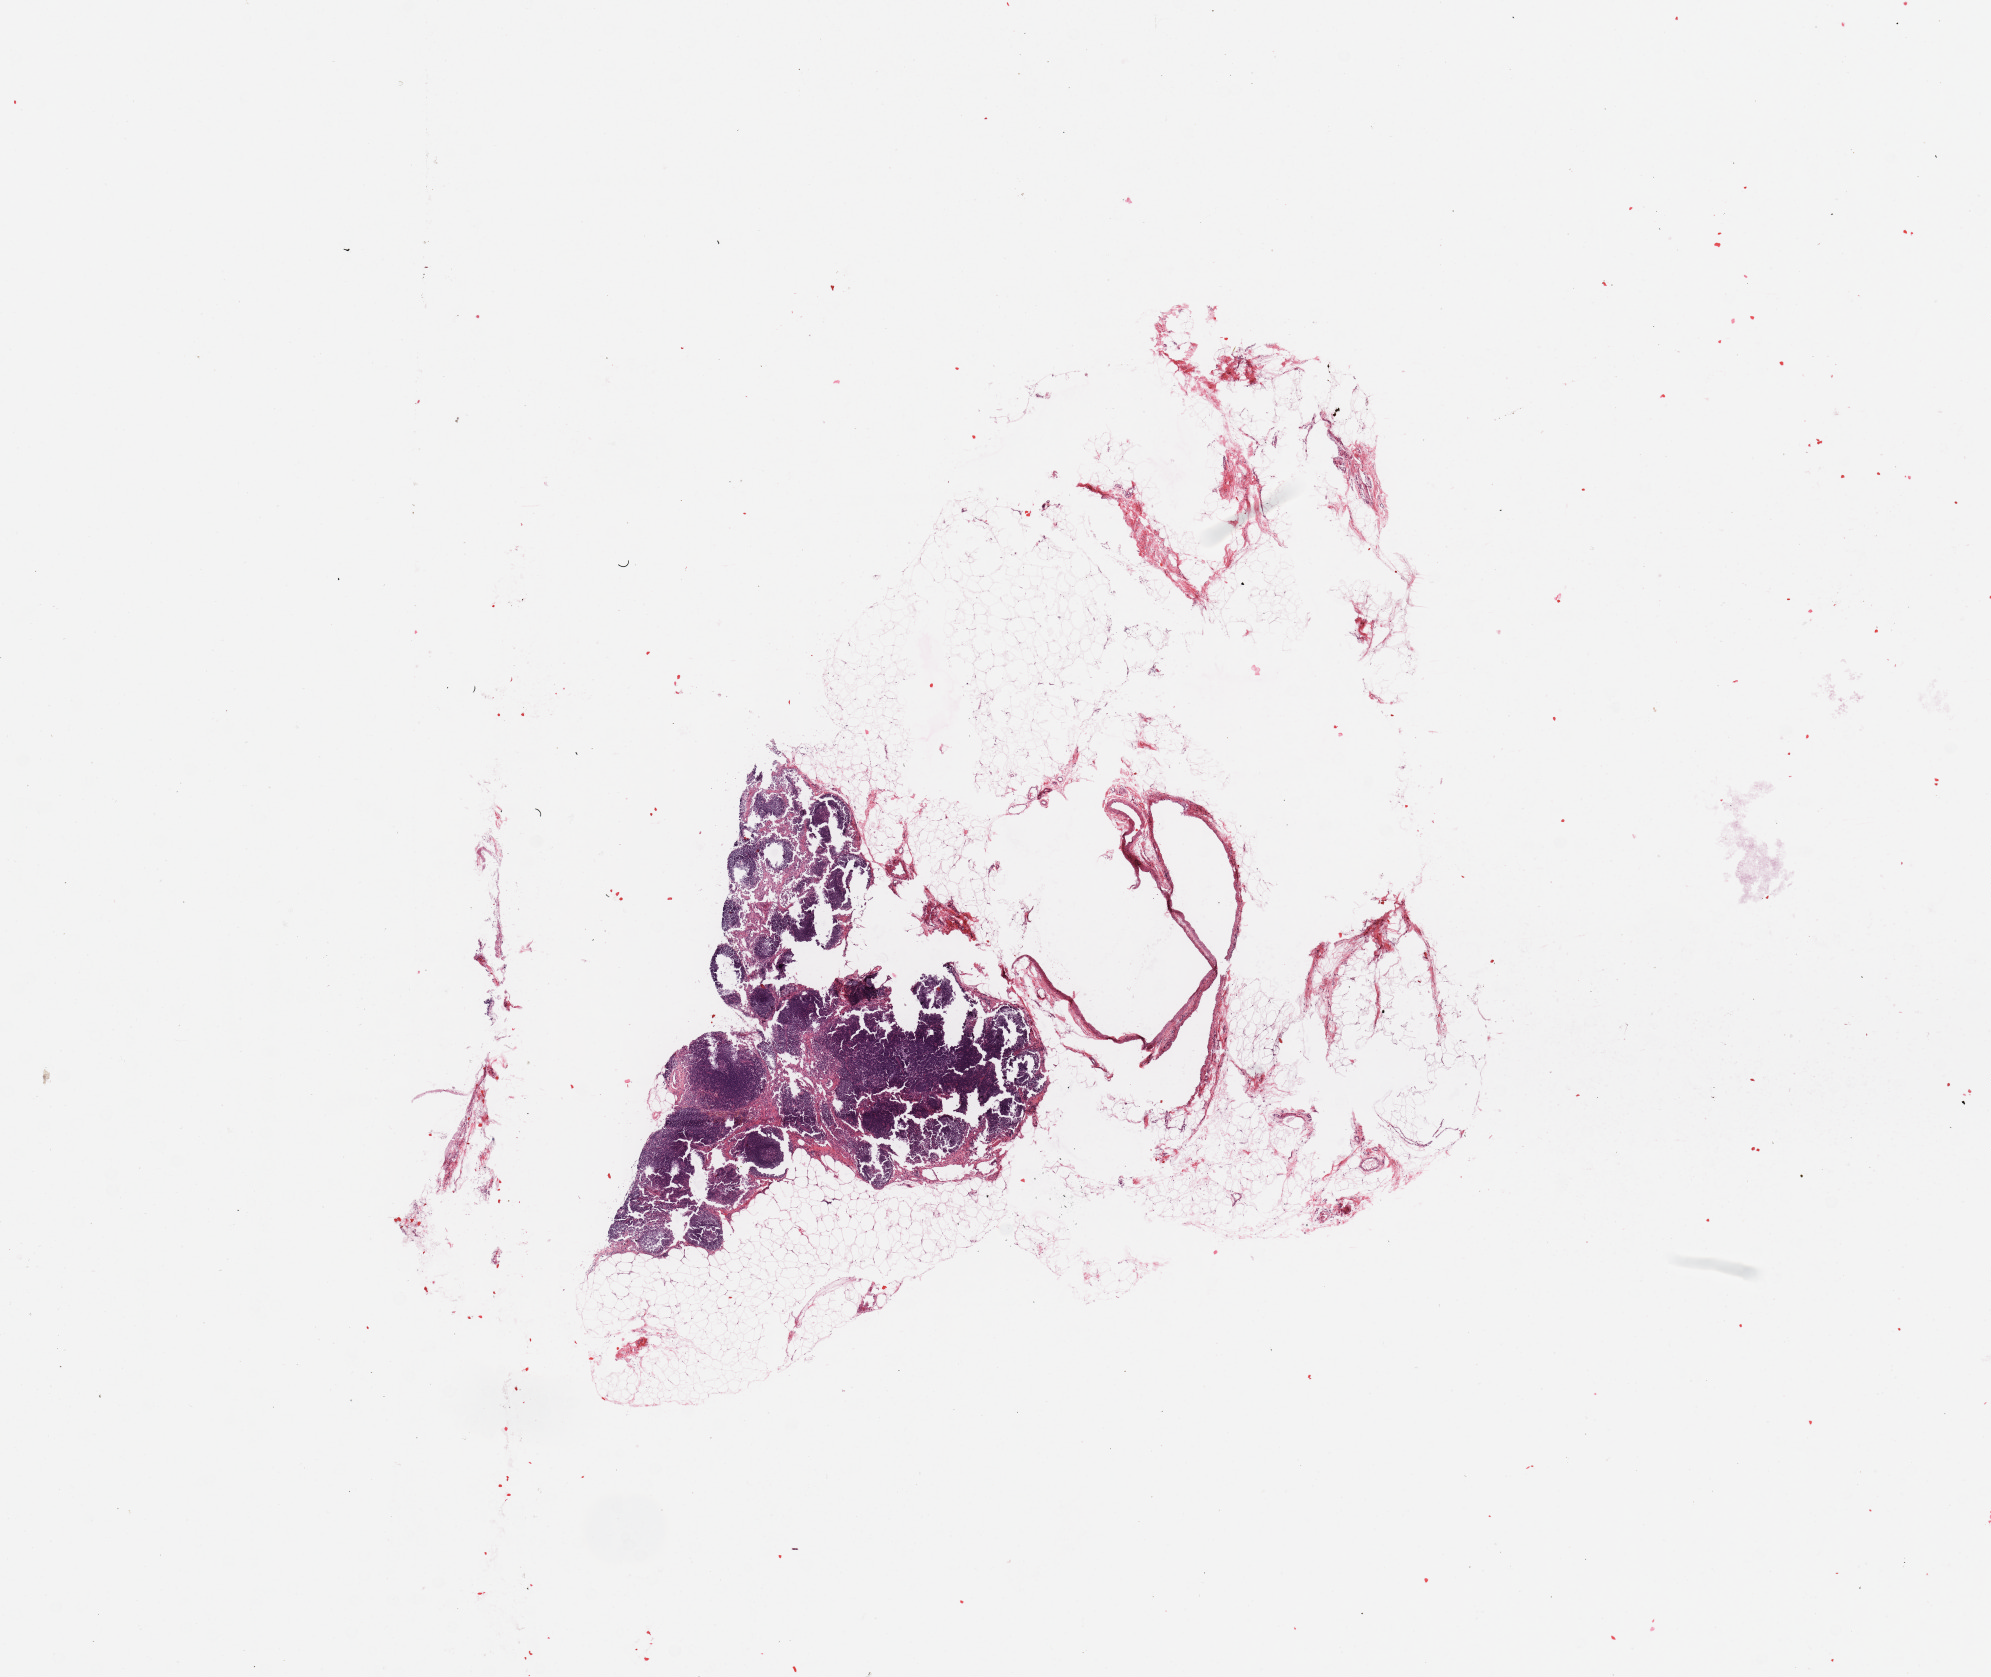
H&E whole-slide image — low-resolution overview of the scanned area, about 15.8 x 13.3 mm. Normal (non-tumour) tissue sample, pancreas. 49-year-old female patient.
* this section: normal (non-tumour) tissue from the same patient
* patient diagnosis: Infiltrating duct carcinoma, NOS